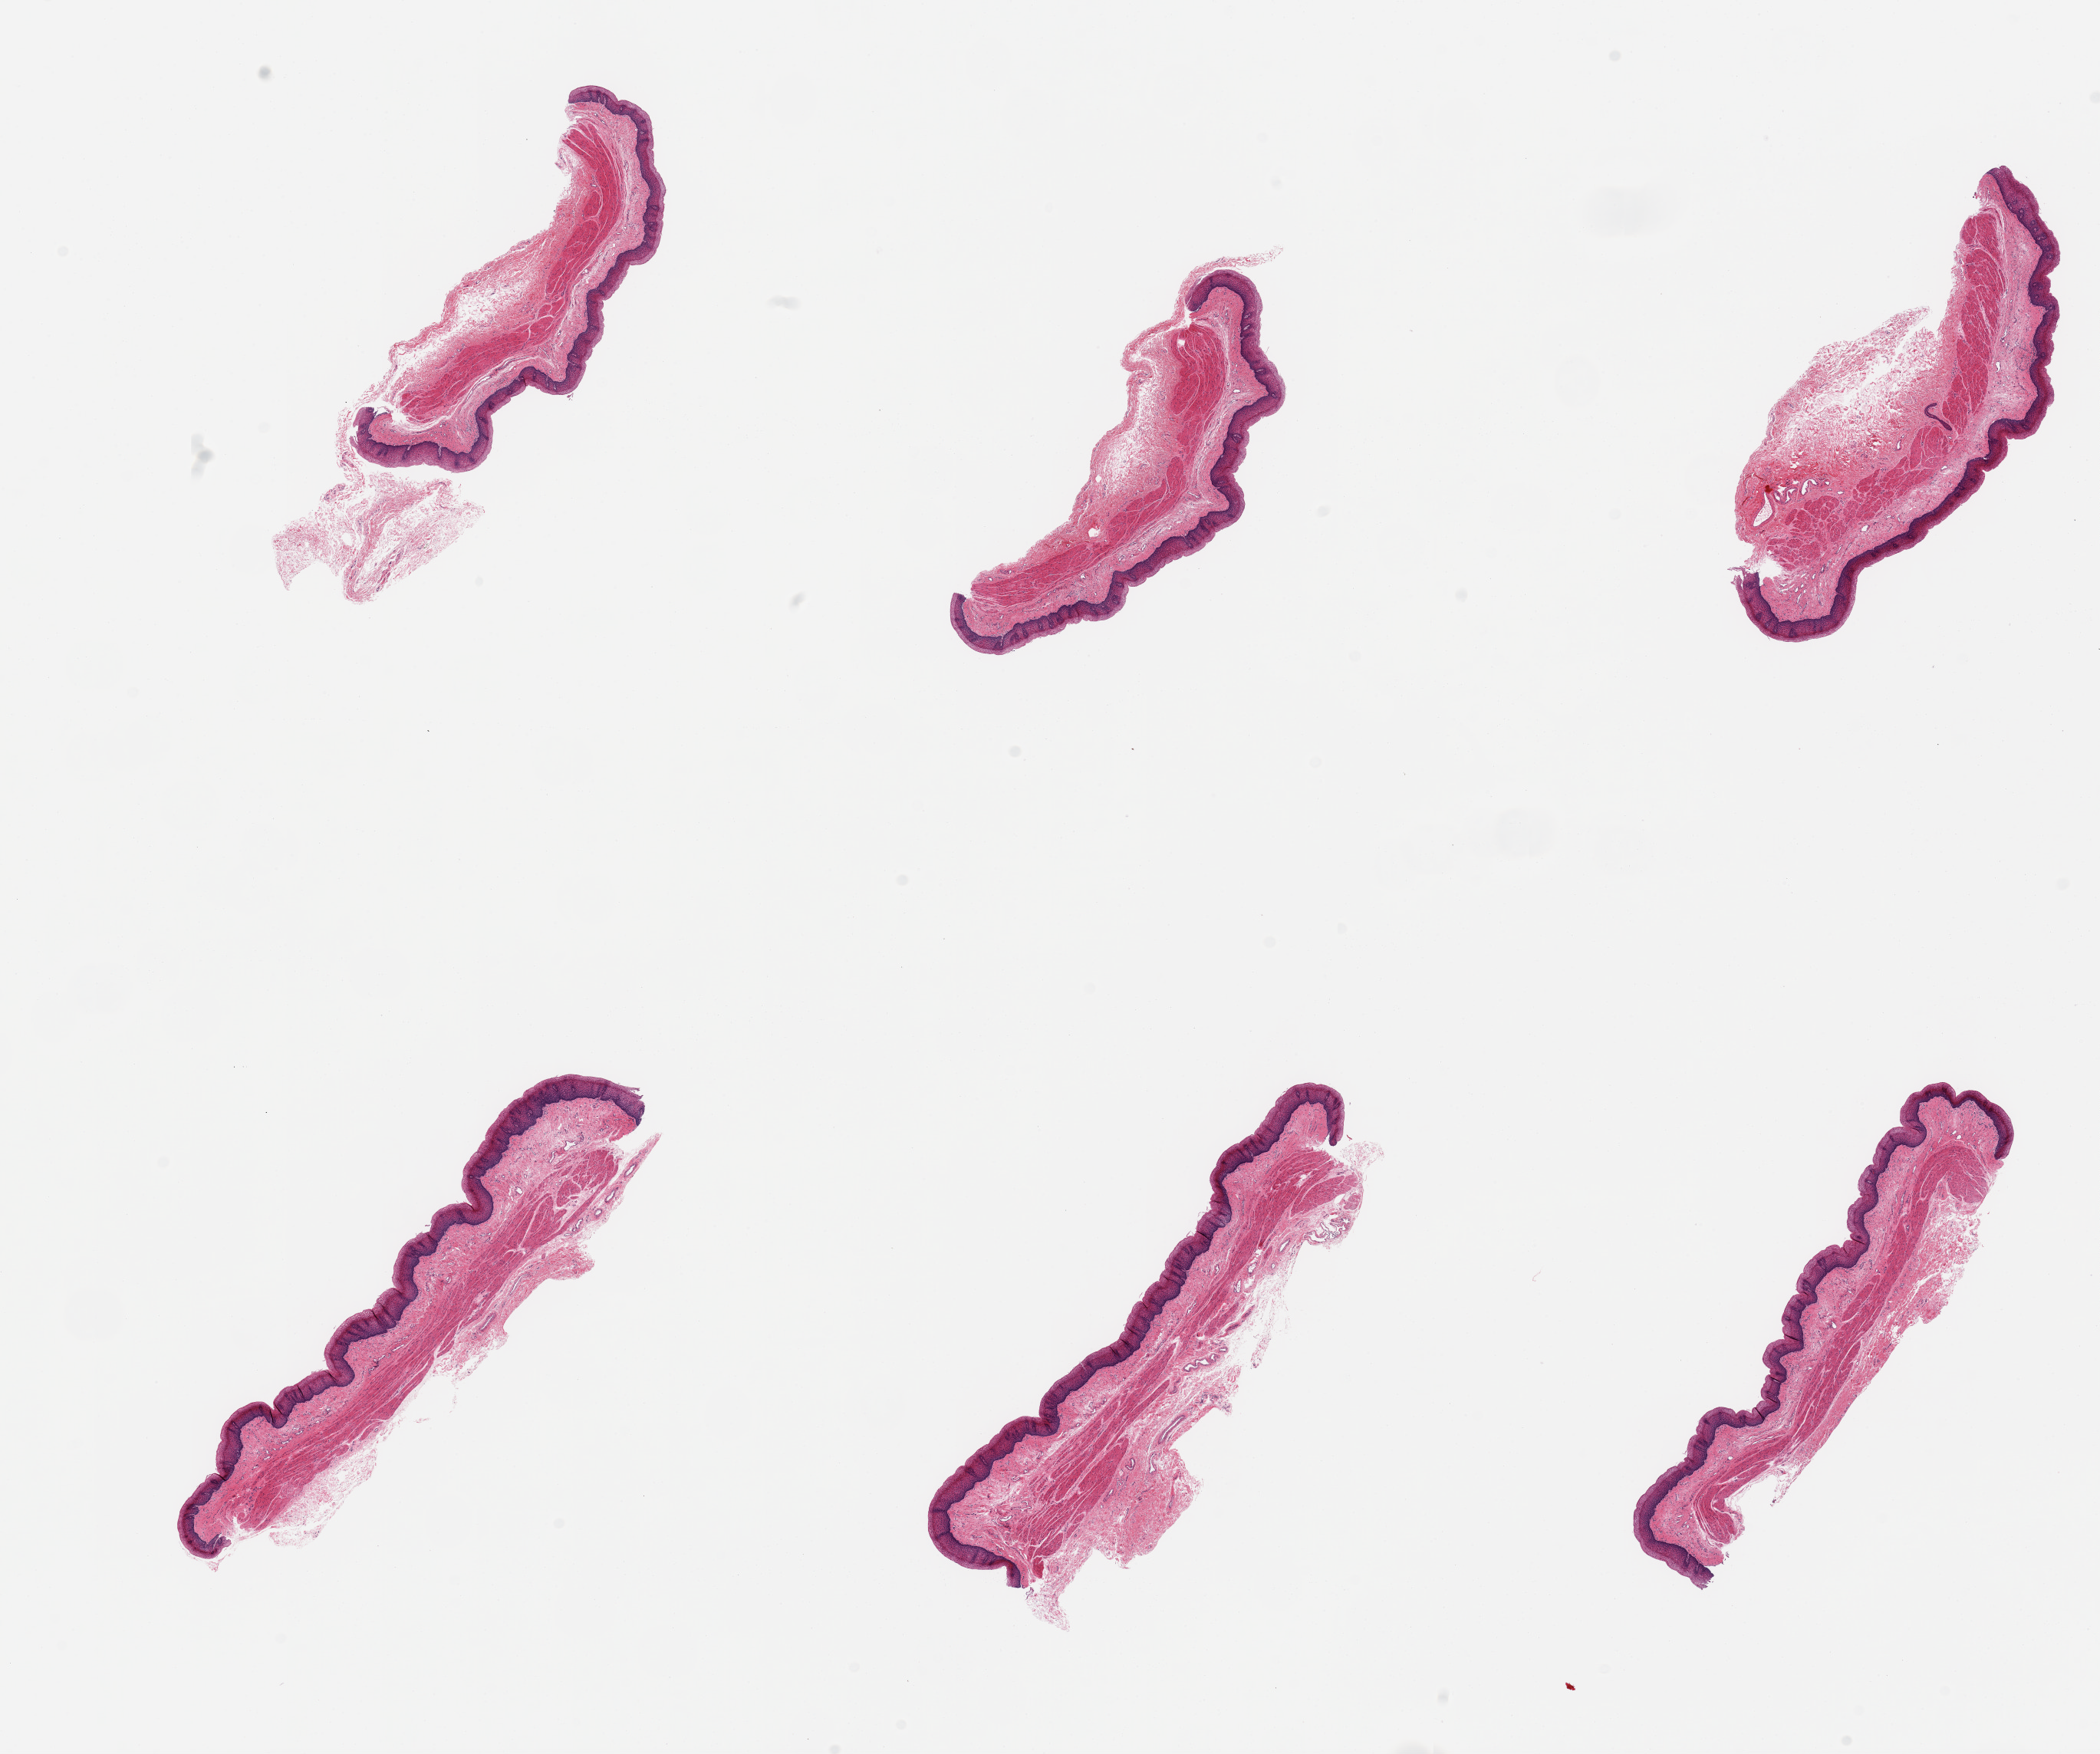
Whole-slide image, hematoxylin and eosin (H&E) stain, brightfield, whole scanned area (about 21.7 x 18.1 mm, acquisition: 20x scan) shown as a low-resolution overview. PAXgene-fixed, paraffin-embedded tissue. Target tissue: esophageal mucous membrane. Tissue donor sample. Donor sex: female.
Reviewer comment on this tissue sample: 6 pieces, squamous mucosa is ~15% thickness.